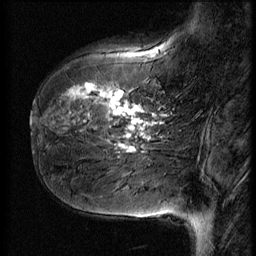
Breast MRI (dynamic contrast-enhanced), one sagittal slice; position 16 of 56 along the scan axis; 3 images stored at this slice position (order not interpretable as contrast timing); 1.5 T; TE 4.2 ms, TR 9 ms; 2.5 mm slice thickness; 256 × 256 image matrix, field of view 180 × 180 mm. Patient: female, 51 years. From the clinical record (not read from this slice): setting: breast cancer imaged before/during neoadjuvant chemotherapy; receptor status: HR-positive, HER2-negative.
Annotated regions visible in this slice (semi-automatic segmentation, software-assisted and operator-edited):
- analysis volume of interest (the breast-tissue region the enhancement analysis was run in; not a lesion): bounding box [x1, y1, x2, y2] px = [41, 58, 167, 161]
- tumour enhancement mask (voxels above the 140 % enhancement threshold inside the analysis volume of interest): [66, 83, 154, 153]